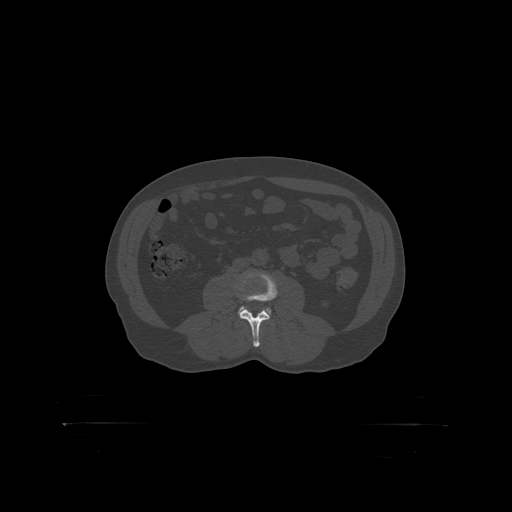
CT including the spine, one axial slice; slice 257 of 399 in the series (ordered by position); reconstruction kernel STANDARD; bone window (W 1800 / L 400 HU); 512 × 512 image matrix, field of view 650 × 650 mm. Male patient, age 46 years. From the clinical record (not read from this slice): primary cancer: skin.
Annotated regions visible in this slice (semi-automatic segmentation, software-assisted and operator-edited):
- L3 vertebra: bounding box [x1, y1, x2, y2] px = [240, 272, 278, 319]
- L4 vertebra: [238, 307, 272, 316]